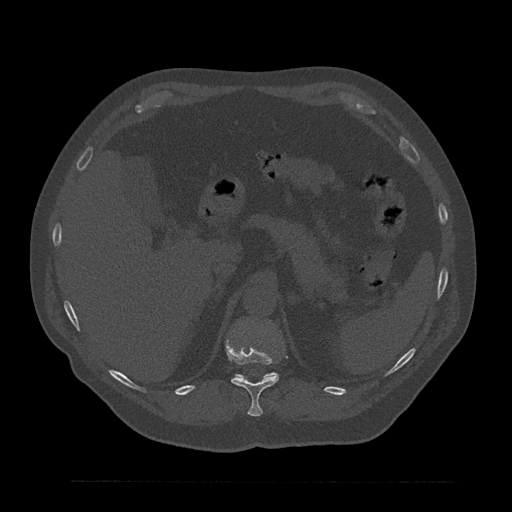
CT including the spine, one axial slice; slice 274 of 797 in the series (ordered by position); reconstruction kernel Br40s/3; 120 kVp; bone window (W 1800 / L 400 HU); 0.5 mm slice thickness; 512 × 512 image matrix, field of view 430 × 430 mm. Patient: male, 61 years. From the clinical record (not read from this slice): primary cancer: prostate.
Structures marked on this image (semi-automatic segmentation, software-assisted and operator-edited):
- T11 vertebra: bounding box <226,339,279,417> (left, top, right, bottom; pixels)
- T12 vertebra: <237,373,277,378>